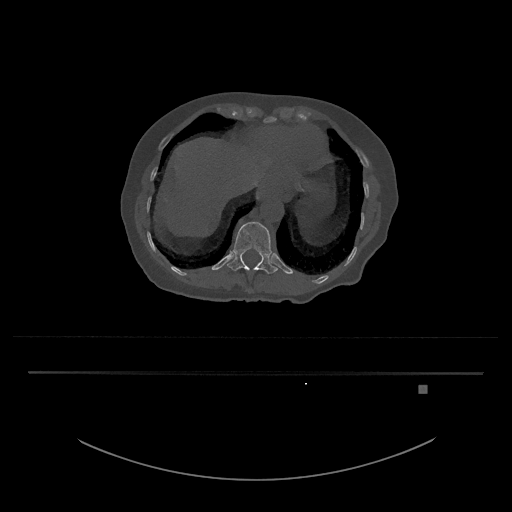
CT including the spine, one axial slice. Position 620 of 797 along the scan axis. Reconstruction kernel Br40s/3. 120 kVp. Bone window (W 1800 / L 400 HU). 0.5 mm slice thickness. 512 × 512 image matrix, field of view 500 × 500 mm. Patient: female, 57 years. From the clinical record (not read from this slice): primary cancer: cervical.
Structures marked on this image (semi-automatic segmentation, software-assisted and operator-edited):
- T12 vertebra: bounding box [x1, y1, x2, y2] px = [227, 222, 278, 274]